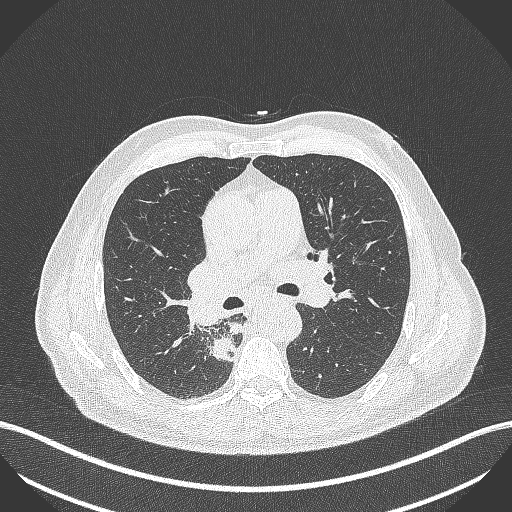
Chest CT, one axial slice; position 276 of 451 along the scan axis; lung window (W 1500 / L -600 HU); 512 × 512 image matrix, field of view 400 × 400 mm. Patient: male, 61 years. From the clinical record (not read from this slice): clinical TNM (as recorded): T1 N0 M0; histopathological grade: G3.
Structures marked on this image (bounding box drawn by a radiologist):
- lung tumour (recorded histology: small cell carcinoma): bounding box (x1, y1, x2, y2) in pixels: (206, 333, 240, 366)